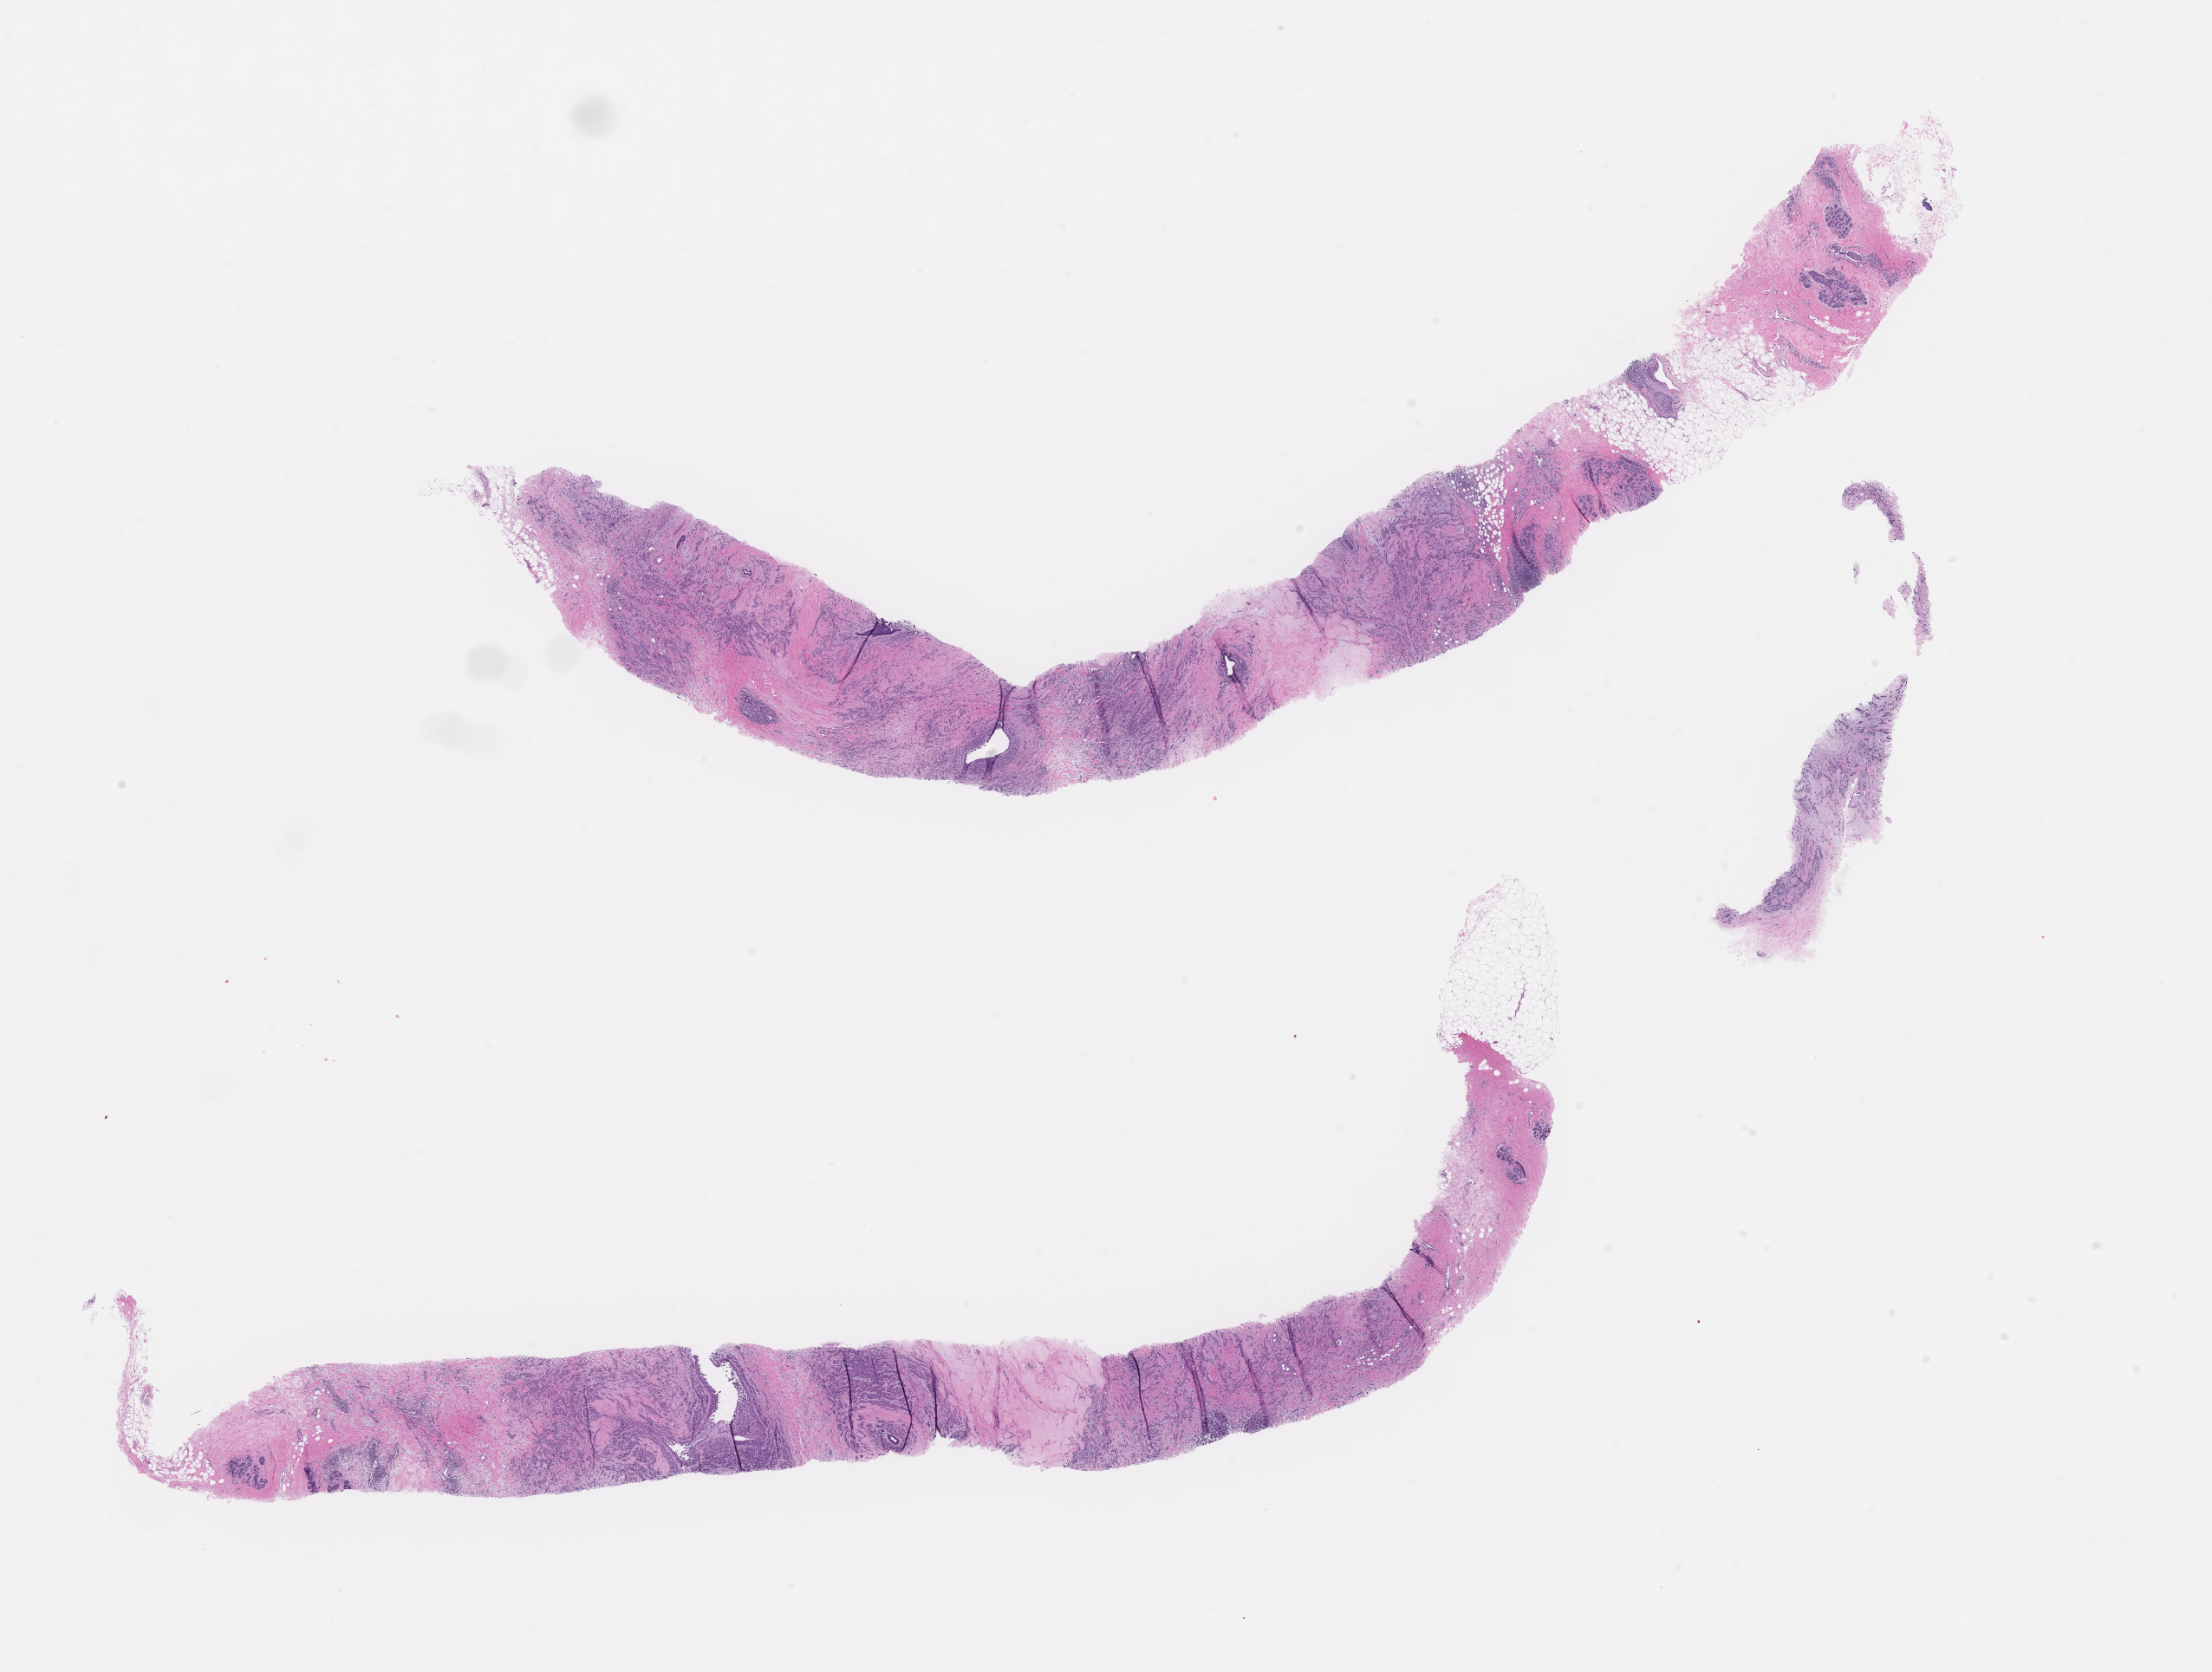
H&E whole-slide image — whole scanned area (about 20.6 x 15.6 mm) shown as a low-resolution overview, formalin-fixed, paraffin-embedded (FFPE) tissue, tissue site: breast, archival tissue. Patient sex: female.
This section: primary tumor. Diagnosis: Invasive Breast Carcinoma.